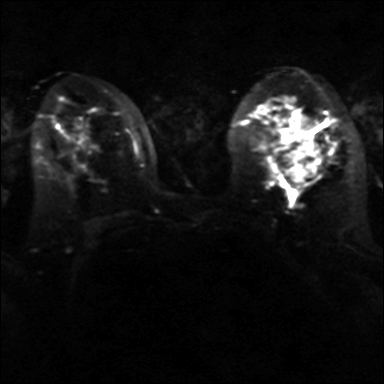
Breast MRI, one axial slice; position 21 of 40 along the scan axis; diffusion-weighted series; image 2 of 4 stored at this slice position (different b-values; order by instance number); 3 T; 4 mm slice thickness; 384 × 384 image matrix, field of view 320 × 320 mm. Female patient.
Annotated regions visible in this slice (manually delineated by an expert):
- tumour on diffusion-weighted imaging: bounding box [x1, y1, x2, y2] px = [284, 142, 321, 183]